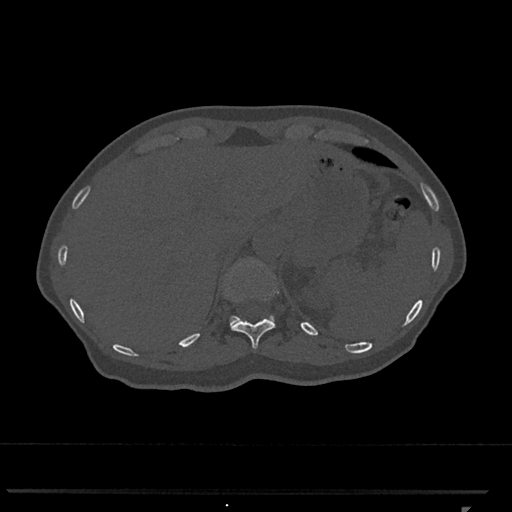
CT including the spine, one axial slice; position 502 of 793 along the scan axis; reconstruction kernel Br40s/3; 120 kVp; bone window (W 1800 / L 400 HU); 0.5 mm slice thickness; 512 × 512 image matrix, field of view 380 × 380 mm. Patient: female, 62 years. From the clinical record (not read from this slice): primary cancer: renal.
Structures marked on this image (semi-automatic segmentation, software-assisted and operator-edited):
- T11 vertebra: bounding box [x1, y1, x2, y2] px = [230, 261, 279, 349]
- T12 vertebra: [227, 264, 274, 325]